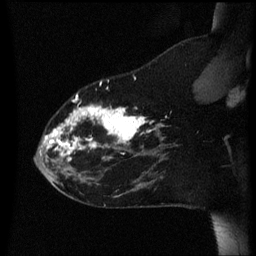
Breast MRI (dynamic contrast-enhanced), one sagittal slice; dynamic contrast-enhanced series, image 2 of 3 at this slice position (ordered by acquisition); 1.5 T; TE 4.2 ms, TR 8.4 ms; 2.2 mm slice thickness; 256 × 256 image matrix, field of view 200 × 200 mm. Female patient, age 35 years. Case-level facts recorded for this patient, not image findings: setting: breast cancer imaged before/during neoadjuvant chemotherapy; receptor status: HER2-positive.
Annotated regions visible in this slice (semi-automatic segmentation, software-assisted and operator-edited):
- analysis volume of interest (the breast-tissue region the enhancement analysis was run in; not a lesion): bounding box (x1, y1, x2, y2) in pixels: (36, 72, 178, 173)
- tumour enhancement mask (voxels above the 70 % enhancement threshold inside the analysis volume of interest): (44, 82, 165, 157)